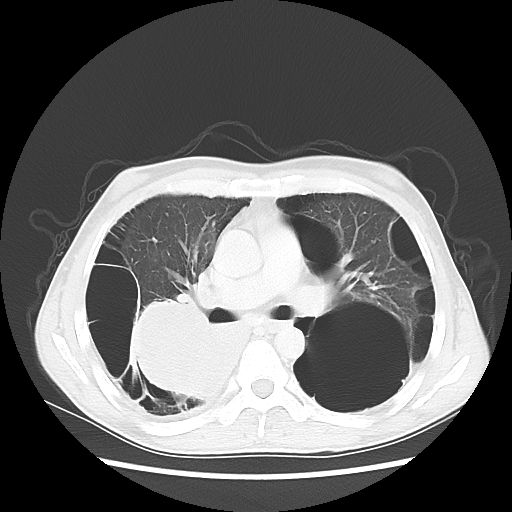
Chest CT, one axial slice. Slice 33 of 57 in the series (ordered by position). Reconstruction kernel LUNG. 140 kVp. Lung window (W 1500 / L -600 HU). 5 mm slice thickness. 512 × 512 image matrix, field of view 351 × 351 mm. Patient: male, 41 years. From the clinical record (not read from this slice): clinical TNM (as recorded): T4 N0 M1a; histopathological grade: G3.
Annotated regions visible in this slice (bounding box drawn by a radiologist):
- lung tumour (recorded histology: large cell carcinoma): bounding box <118,295,240,399> (left, top, right, bottom; pixels)